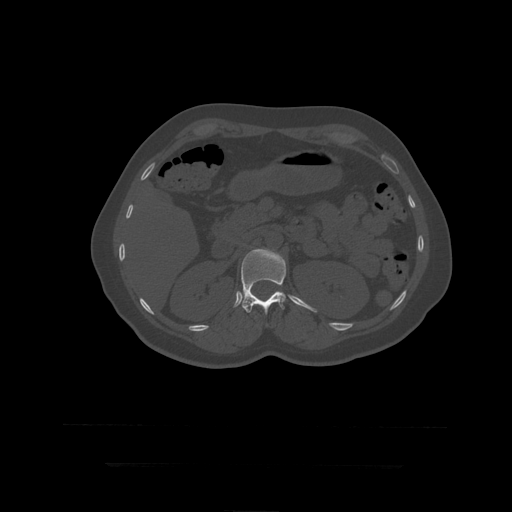
CT including the spine, one axial slice; slice 173 of 399 in the series (ordered by position); 120 kVp; bone window (W 1800 / L 400 HU); 1.25 mm slice thickness; 512 × 512 image matrix, field of view 450 × 450 mm. Patient age 41 years. Case-level facts recorded for this patient, not image findings: primary cancer: breast.
Outlined on this slice (semi-automatically segmented with operator editing):
- L1 vertebra: bounding box <241,249,286,315> (left, top, right, bottom; pixels)